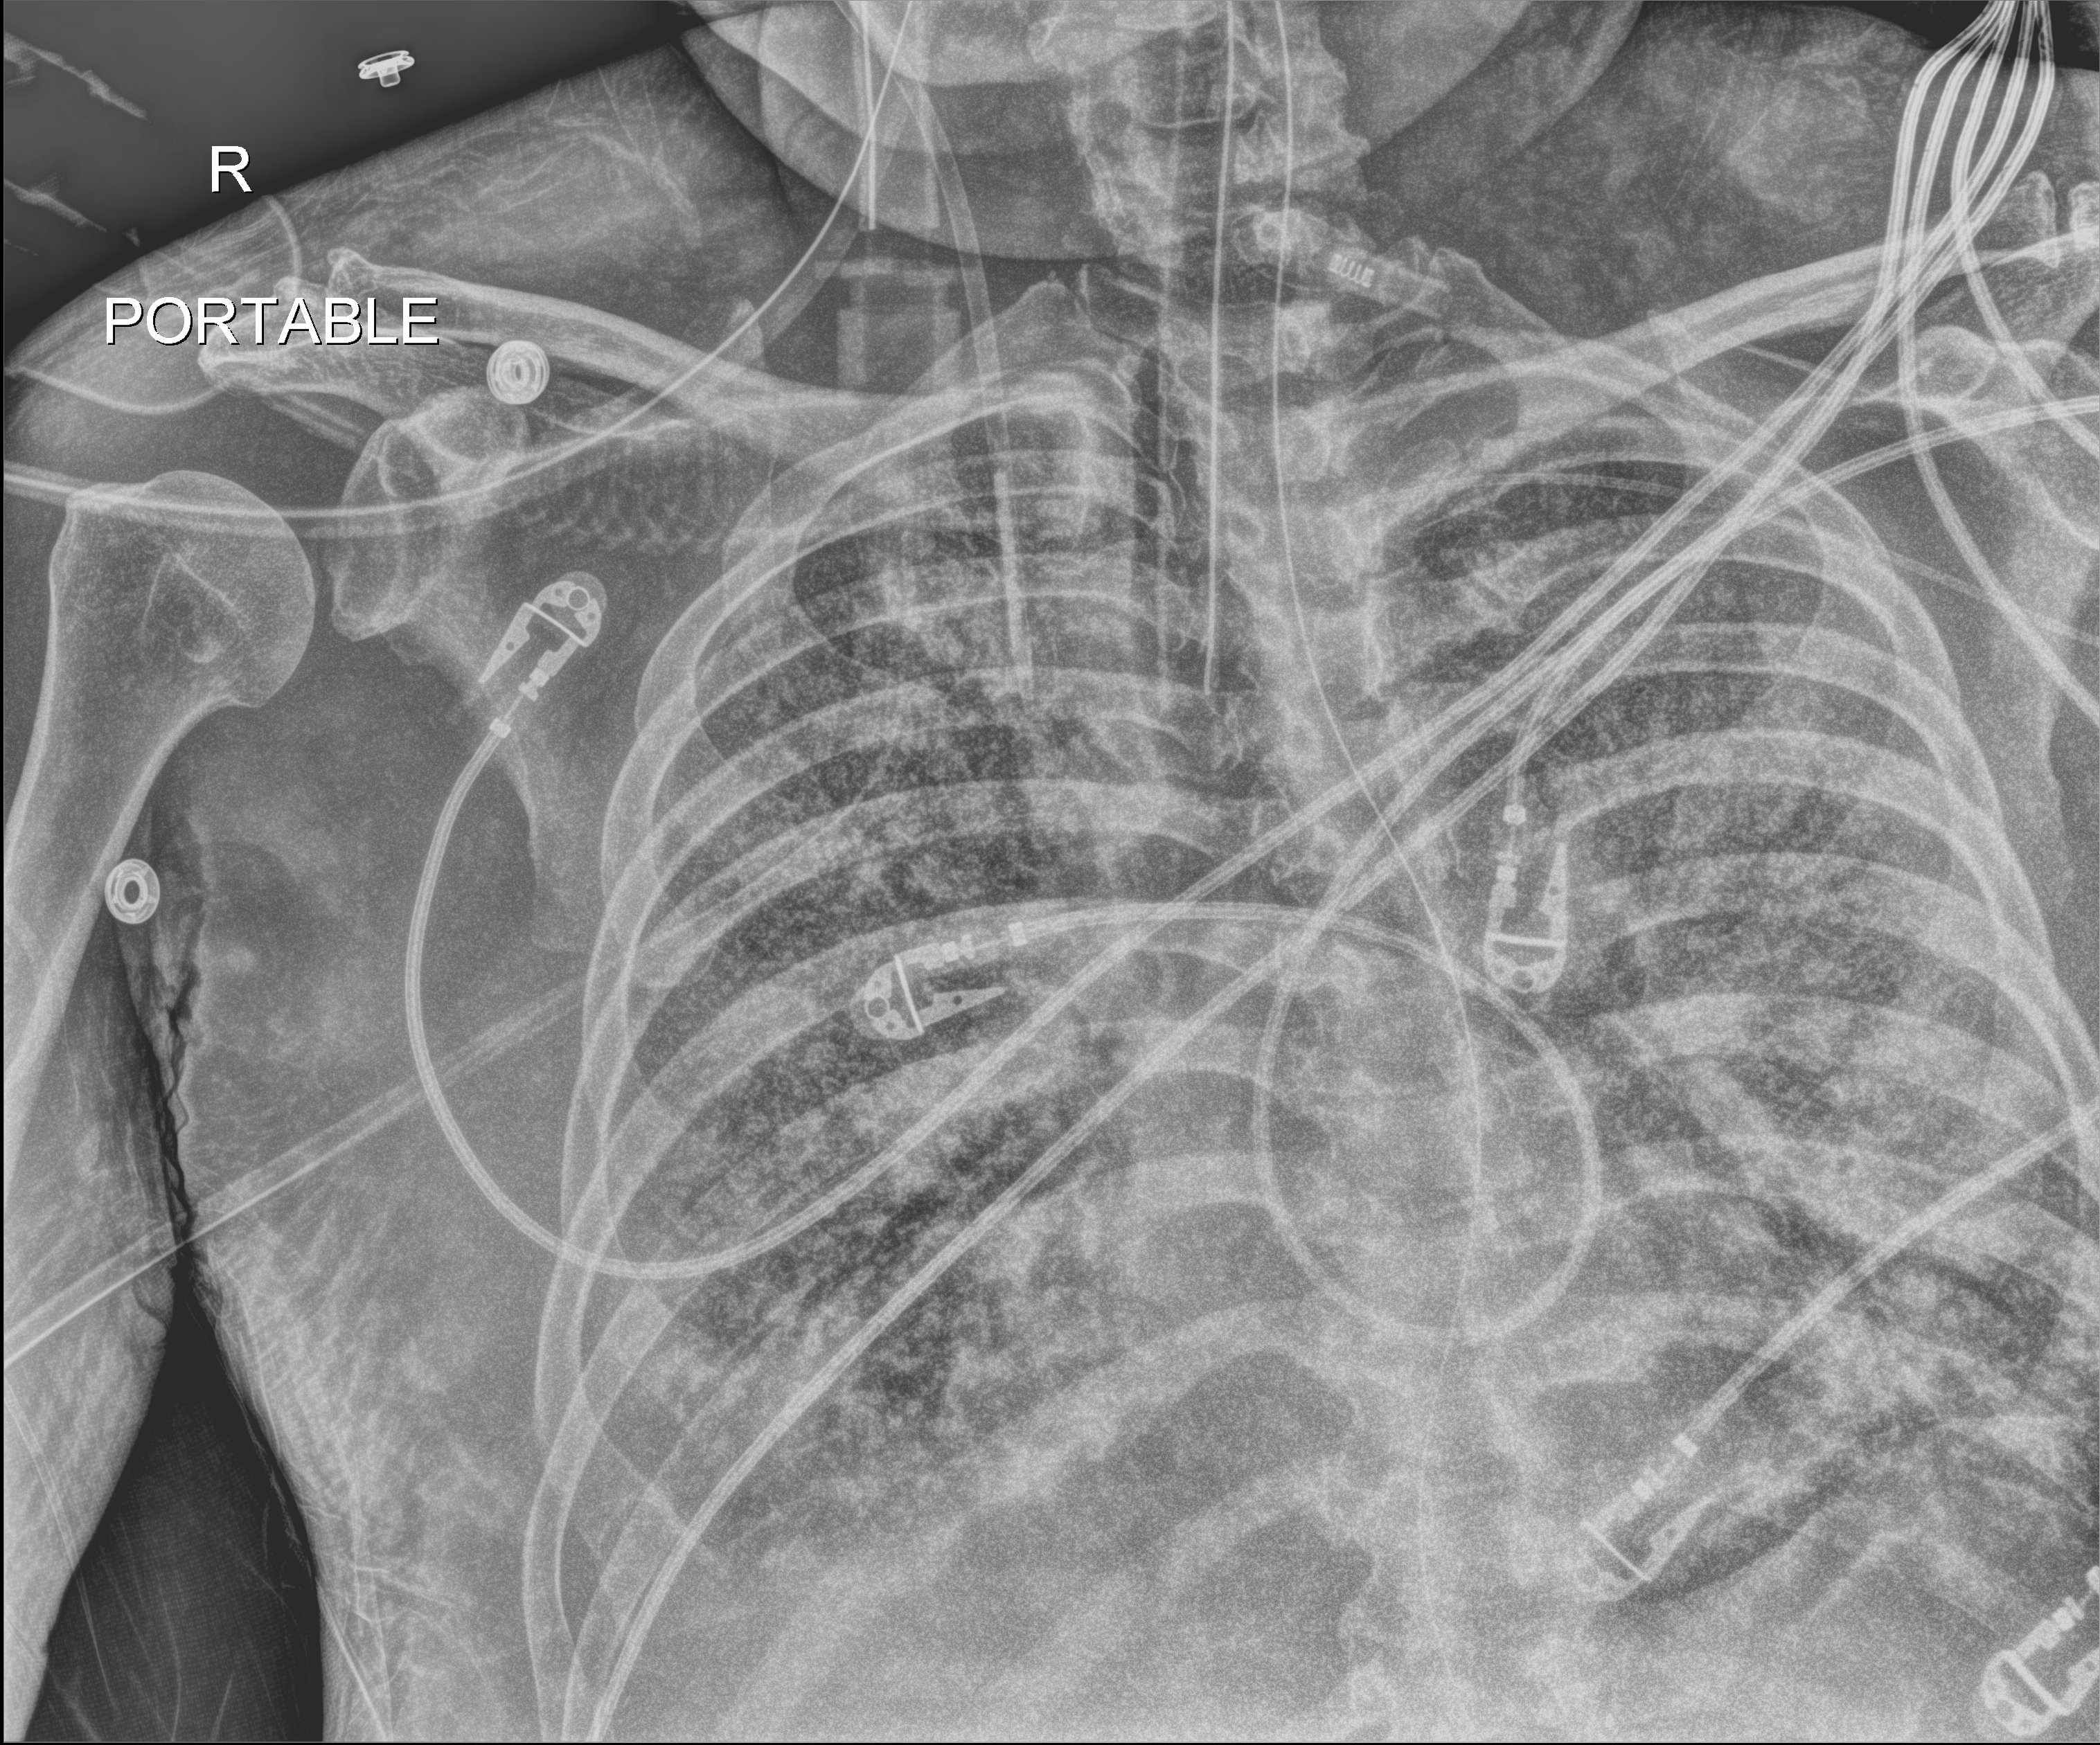
Bedside chest radiograph (digital radiography); anteroposterior (AP) projection. Patient hospitalised with COVID-19; male, aged 60–74 years.
From the hospital-stay record, not from the radiograph (when in the stay this image was taken is not recorded):
- smoking status (admission record): never
- mechanically ventilated during this hospital stay: yes
- admitted to intensive care during this hospital stay: yes